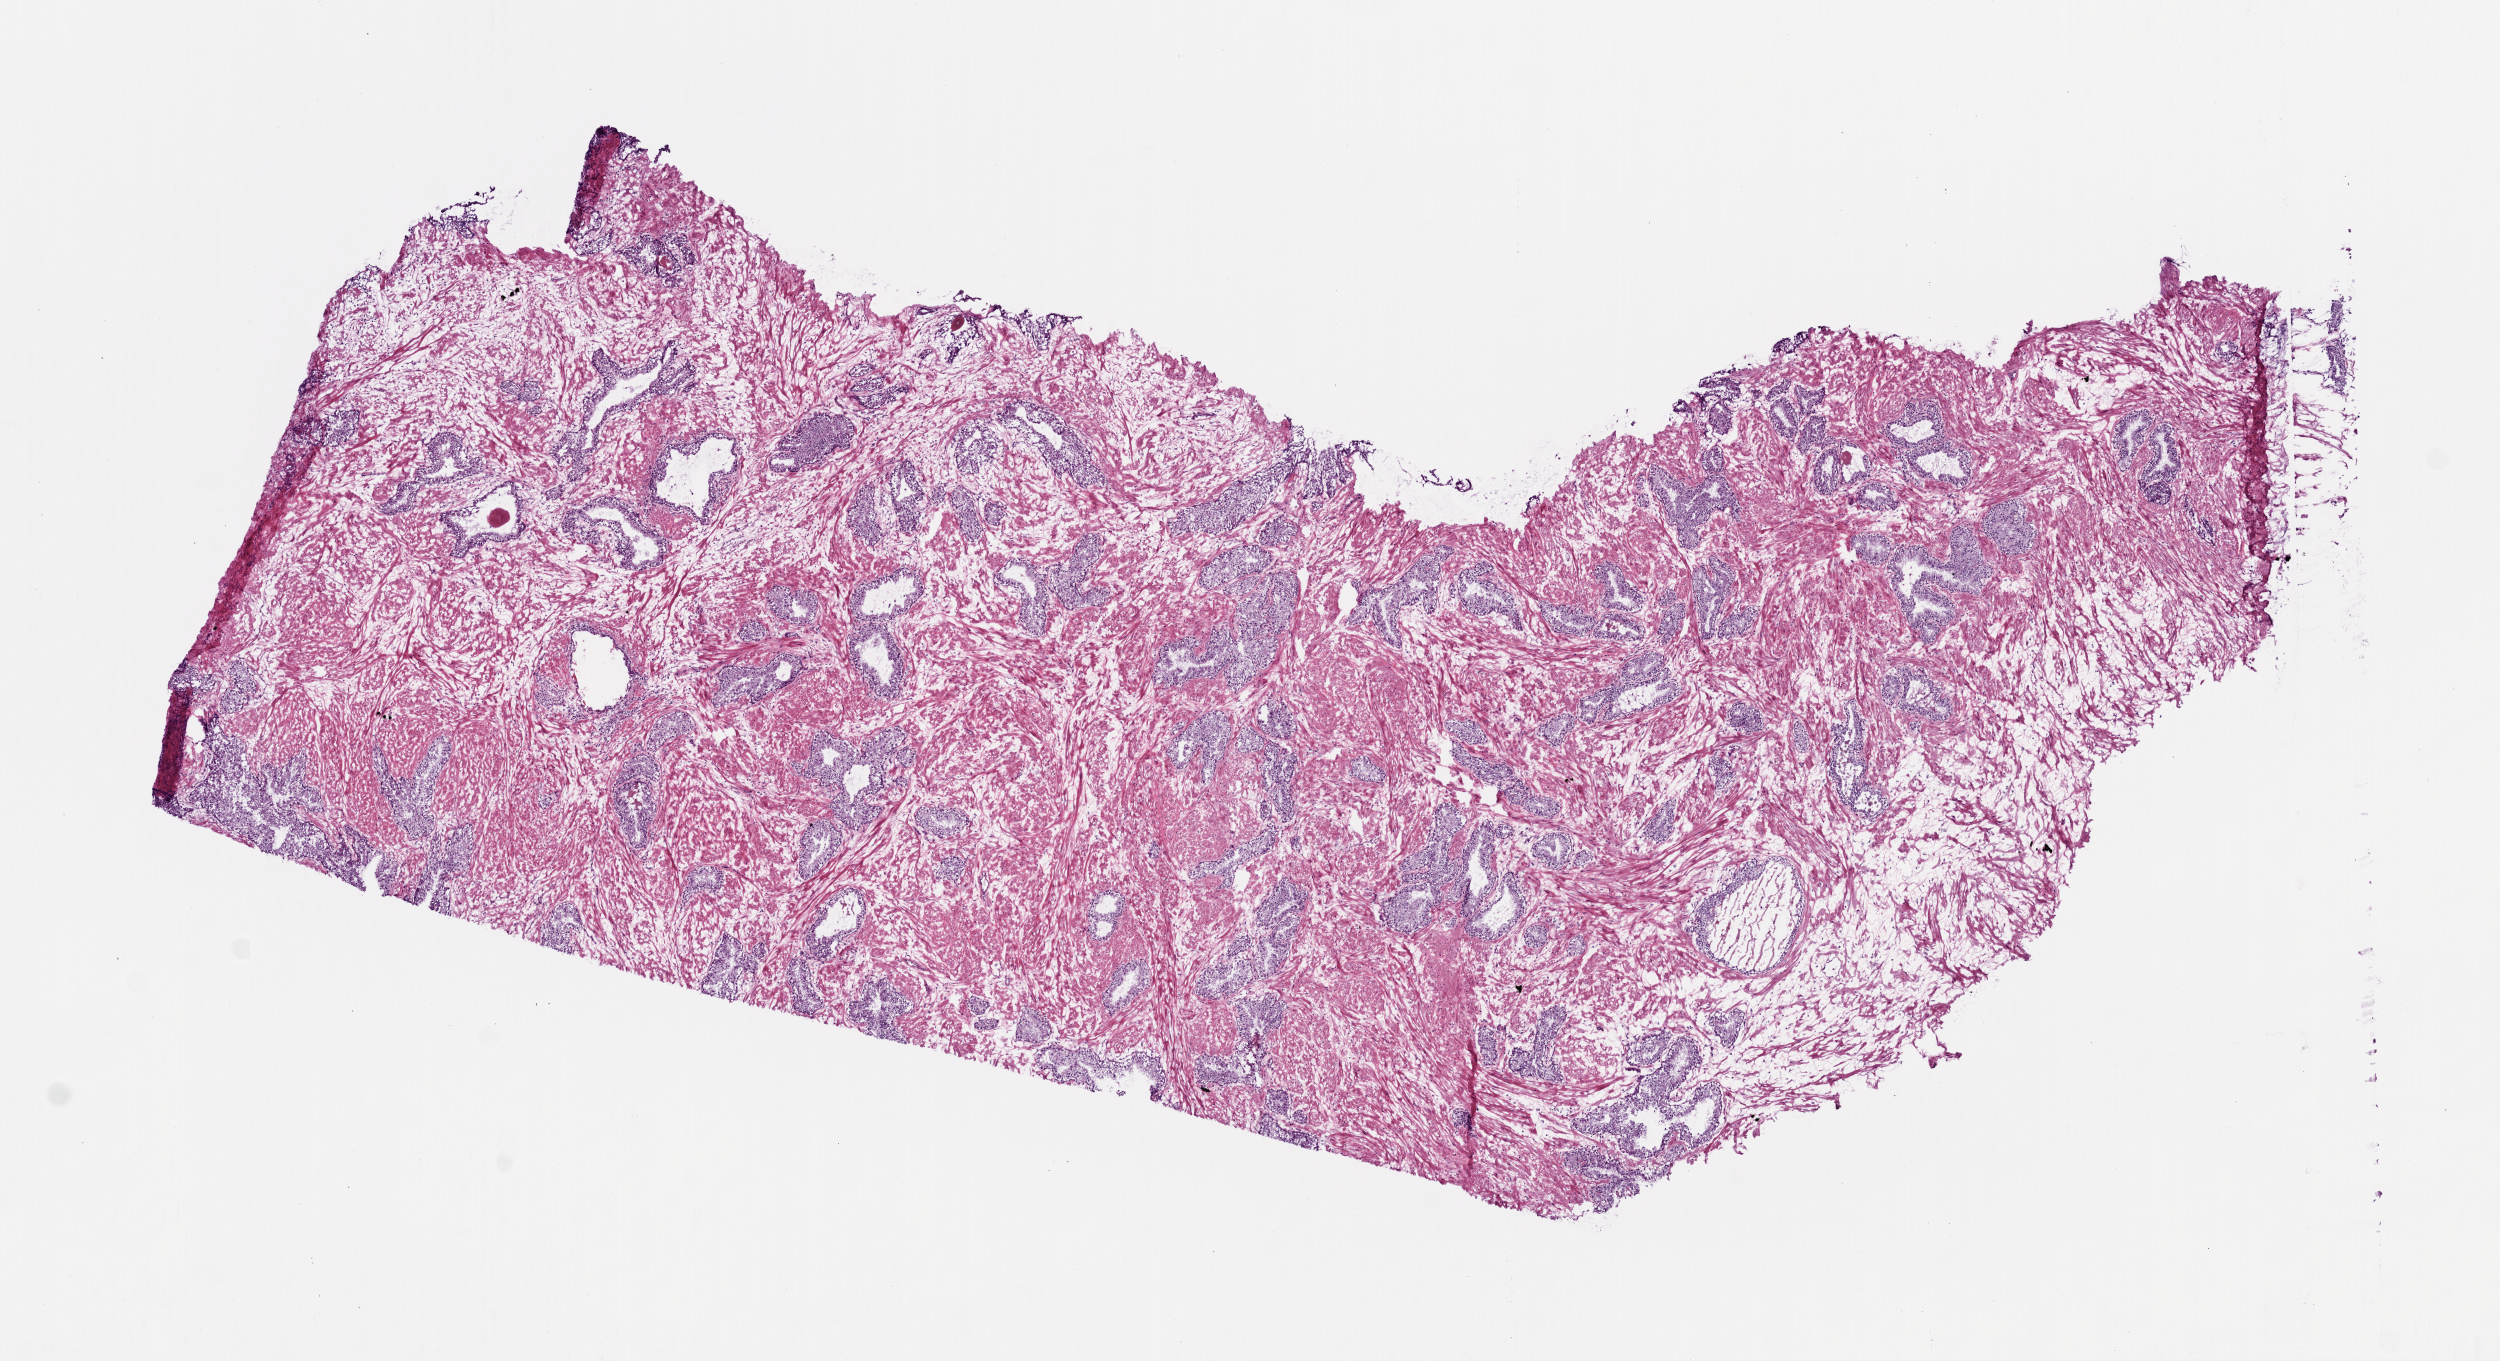
Whole-slide histology image, H&E, shown as a low-resolution overview of the whole scanned area (about 10.0 x 5.5 mm, acquisition: 20x scan), frozen section from the top of the tissue portion, sample: solid tissue normal (non-tumour tissue), prostate. Patient: male, age at initial diagnosis 55 years.
This section: solid tissue normal (non-tumour) sample from the same patient. Patient diagnosis: Acinar cell carcinoma (prostate gland).